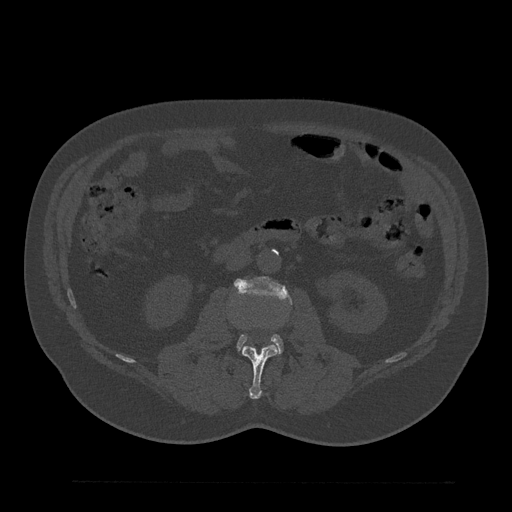
CT including the spine, one axial slice; position 71 of 797 along the scan axis; reconstruction kernel Br40s/3; 120 kVp; bone window (W 1800 / L 400 HU); 0.5 mm slice thickness; 512 × 512 image matrix. Male patient, age 61 years. Case-level facts recorded for this patient, not image findings: primary cancer: prostate.
Outlined on this slice (semi-automatically segmented with operator editing):
- L2 vertebra: bounding box (x1, y1, x2, y2) in pixels: (242, 345, 277, 399)
- L3 vertebra: (234, 277, 287, 352)